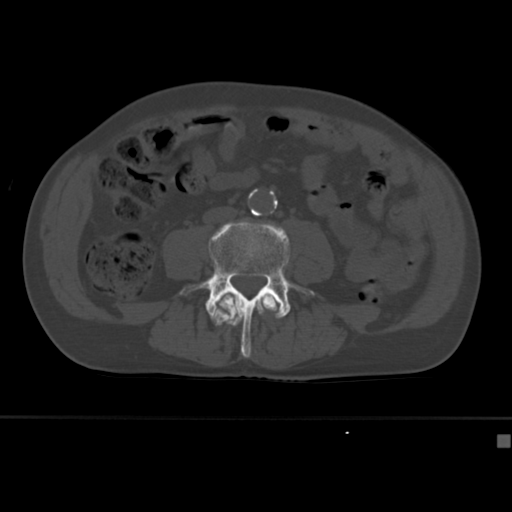
CT including the spine, one axial slice; position 111 of 430 along the scan axis; bone window (W 1800 / L 400 HU); 512 × 512 image matrix, field of view 337 × 337 mm. Patient: male, 64 years. Case-level facts recorded for this patient, not image findings: primary cancer: uterus; vertebrae with lytic lesions (as recorded): T1, T4, T5, T7, L5.
Outlined on this slice (semi-automatically segmented with operator editing):
- L3 vertebra: bounding box (x1, y1, x2, y2) in pixels: (216, 292, 277, 311)
- L4 vertebra: (180, 219, 315, 358)